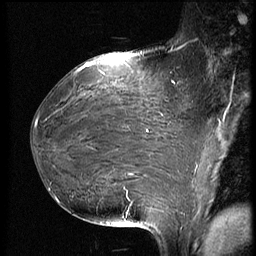
Breast MRI (dynamic contrast-enhanced), one sagittal slice; slice 31 of 66 in the series (ordered by position); dynamic contrast-enhanced series, image 2 of 3 at this slice position (ordered by acquisition); 1.5 T; TE 4.2 ms, TR 8.9 ms; 256 × 256 image matrix, field of view 200 × 200 mm. Female patient, age 39 years. Case-level facts recorded for this patient, not image findings: setting: breast cancer imaged before/during neoadjuvant chemotherapy; receptor status: HER2-positive.
Outlined on this slice (semi-automatic segmentation, software-assisted and operator-edited):
- analysis volume of interest (the breast-tissue region the enhancement analysis was run in; not a lesion): bounding box <32,75,188,218> (left, top, right, bottom; pixels)
- tumour enhancement mask (voxels above the 140 % enhancement threshold inside the analysis volume of interest): <35,125,148,204>